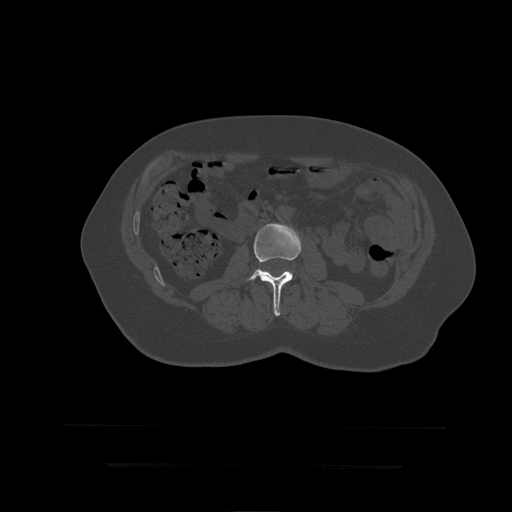
CT including the spine, one axial slice. Slice 121 of 399 in the series (ordered by position). Reconstruction kernel STANDARD. 120 kVp. Bone window (W 1800 / L 400 HU). 1.25 mm slice thickness. 512 × 512 image matrix, field of view 450 × 450 mm. Patient age 41 years. Case-level facts recorded for this patient, not image findings: primary cancer: breast.
Annotated regions visible in this slice (semi-automatic segmentation, software-assisted and operator-edited):
- L3 vertebra: bounding box (x1, y1, x2, y2) in pixels: (247, 224, 302, 316)